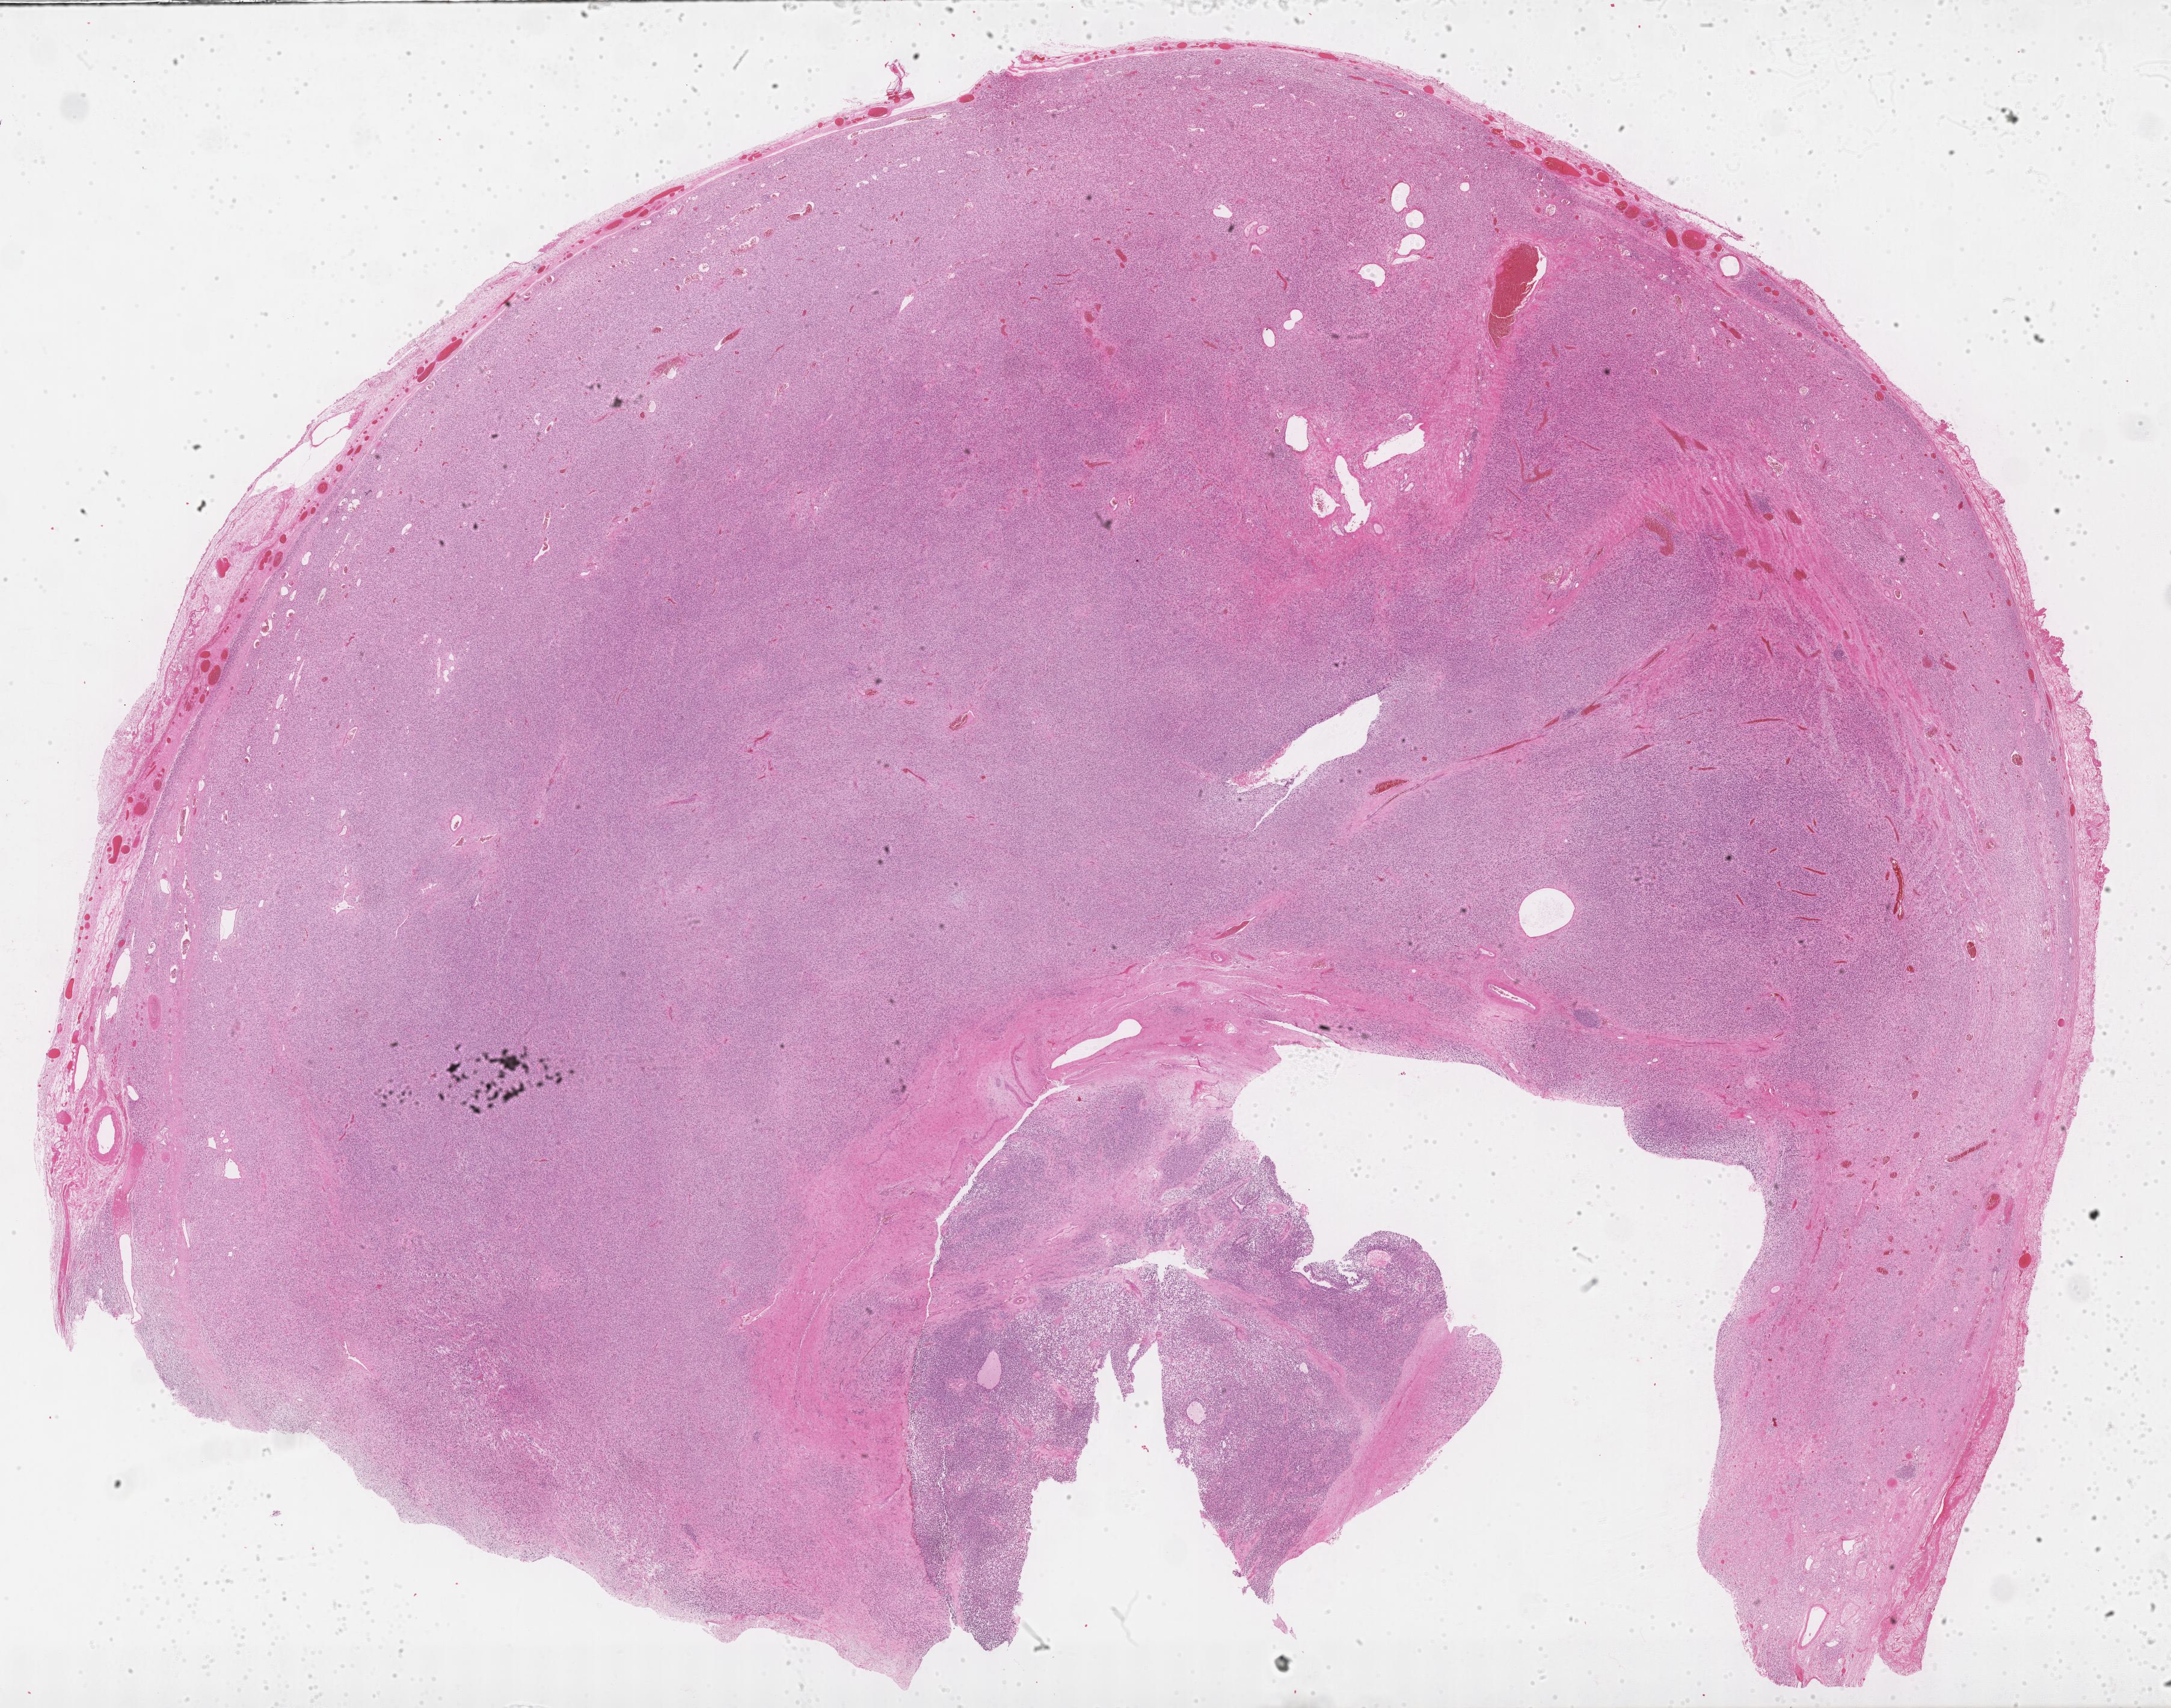
Digitized hematoxylin and eosin (H&E)-stained section of tumor tissue — low-resolution overview of the scanned area, about 29.2 x 23.0 mm; formalin-fixed, paraffin-embedded (FFPE) tissue; site: testicle, right. Patient: male, age 15.2 years at diagnosis.
* stage (as recorded): 1
* diagnosis: rhabdomyosarcoma; histological classification: embryonal rhabdomyosarcoma